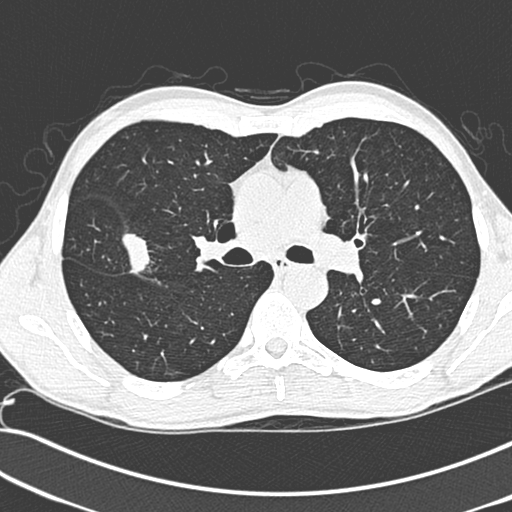
Low-dose screening chest CT, one axial slice; 120 kVp; lung window (W 1500 / L -600 HU); 1.3 mm slice thickness; 512 × 512 image matrix, field of view 341 × 341 mm.
Annotated regions visible in this slice (outlined manually by an expert reader):
- lesion 1 (tumor, upper lobe of right lung): bounding box <122,233,153,275> (left, top, right, bottom; pixels)